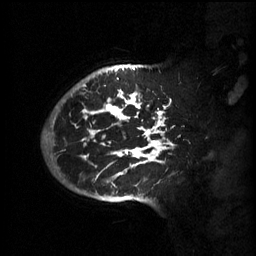
Breast MRI (dynamic contrast-enhanced), one sagittal slice; position 47 of 60 along the scan axis; 3 images stored at this slice position (order not interpretable as contrast timing); 1.5 T; TE 4.2 ms, TR 11 ms; 2 mm slice thickness; 256 × 256 image matrix, field of view 220 × 220 mm. Patient: female, 51 years.
Outlined on this slice (semi-automatically segmented with operator editing):
- analysis volume of interest (the breast-tissue region the enhancement analysis was run in; not a lesion): bounding box (x1, y1, x2, y2) in pixels: (63, 80, 180, 201)
- tumour enhancement mask (voxels above the 70 % enhancement threshold inside the analysis volume of interest): (71, 84, 174, 187)